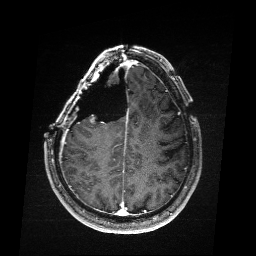
Brain MRI from a brain-tumour surgery series, one axial slice; position 66 of 176 along the scan axis; T1-weighted post-contrast; 256 × 256 image matrix, field of view 256 × 256 mm. From the clinical record (not read from this slice): histopathology: Astrocytoma; WHO grade: 4; IDH mutation: yes.
Outlined on this slice (outlined manually by an expert reader):
- residual tumour: bounding box (x1, y1, x2, y2) in pixels: (90, 117, 95, 123)